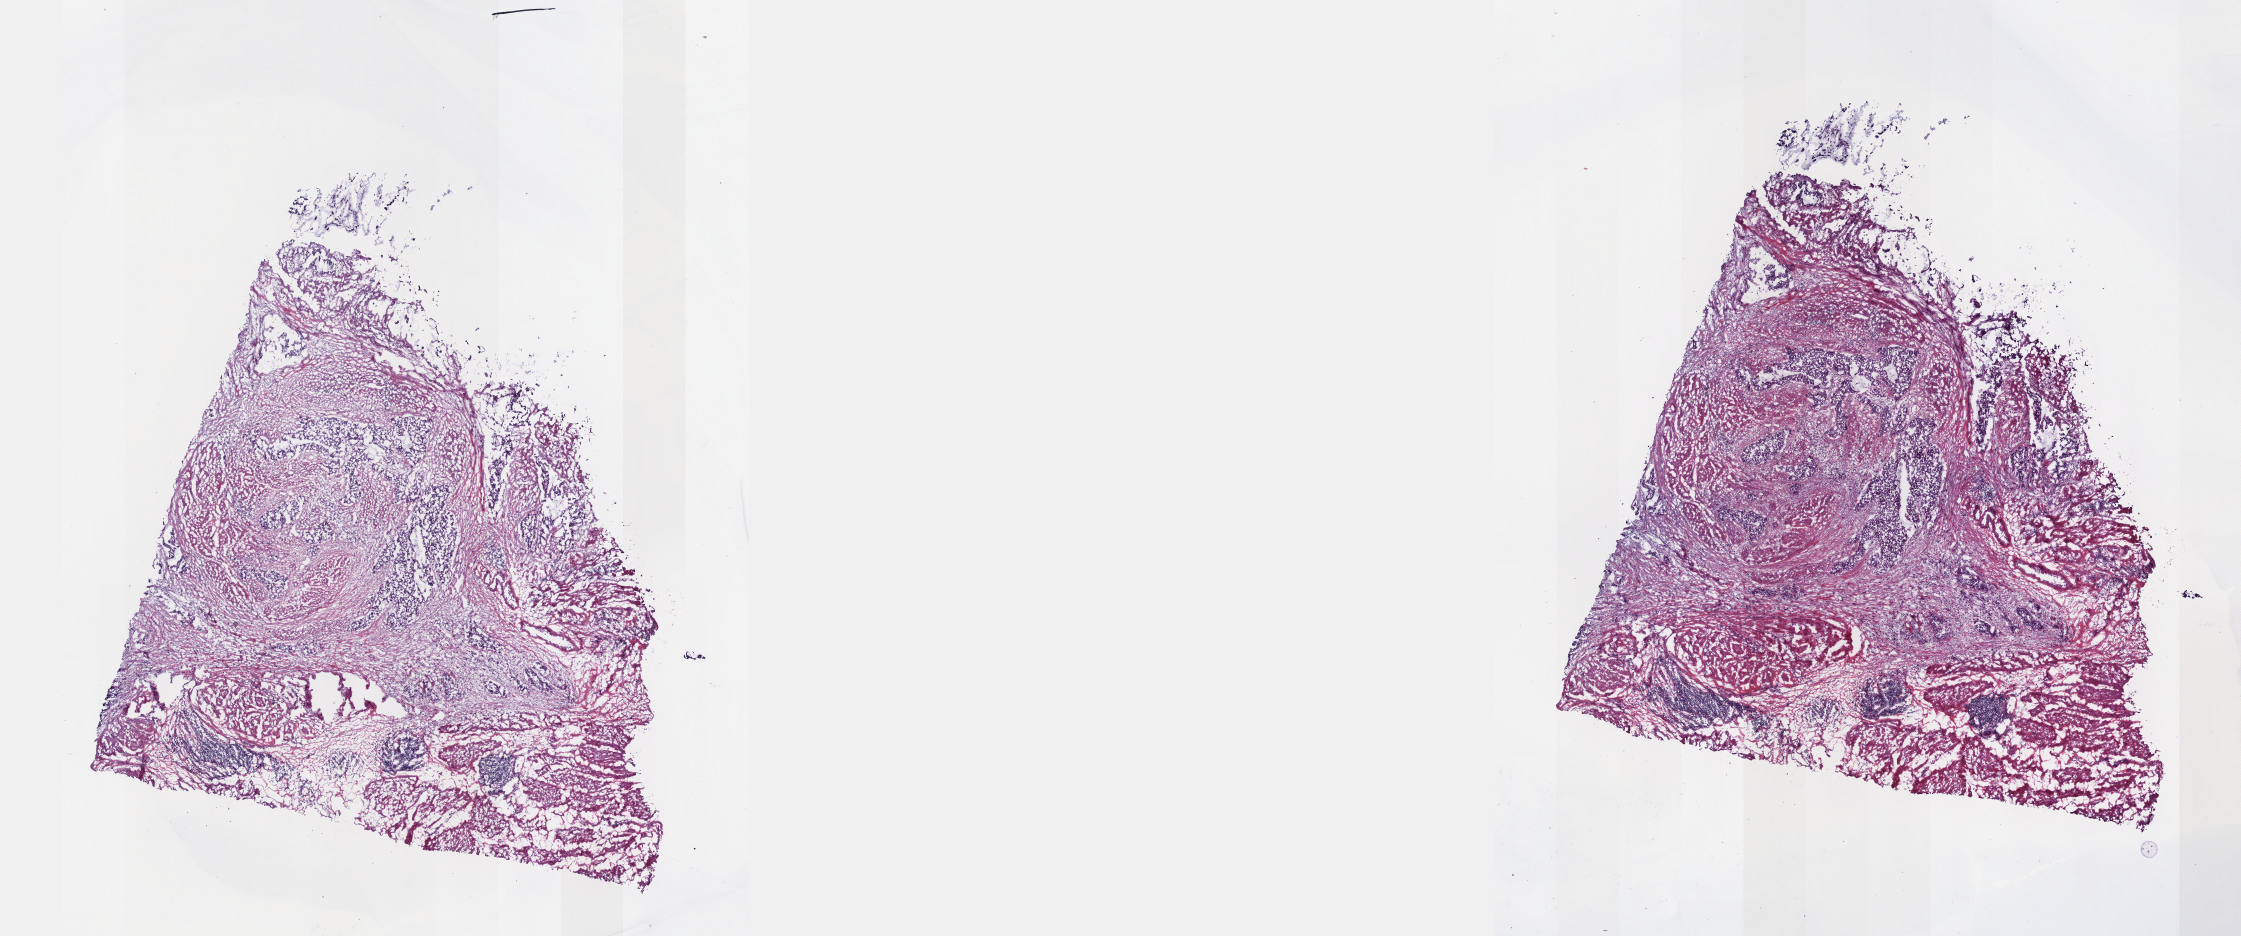
Whole-slide histology image, H&E — shown as a low-resolution overview of the whole scanned area (about 18.1 x 7.6 mm, from a 40x scan); frozen section from the top of the tissue portion; bladder, primary tumour sample. Male, age 81 years at initial diagnosis. Histologic grade: high grade. Composition of this section per pathologist review: tumour cells 70%, tumour nuclei 70%, normal cells 0%, stromal cells 30%, necrosis 0%. Inflammatory infiltration, as recorded: lymphocyte infiltration 2%, monocyte infiltration 1%, neutrophil infiltration 3%.
AJCC pathologic stage: IV (7th edition). Lymph nodes positive (case pathology): 2 of 13 examined. Pathologic diagnosis: Transitional cell carcinoma.